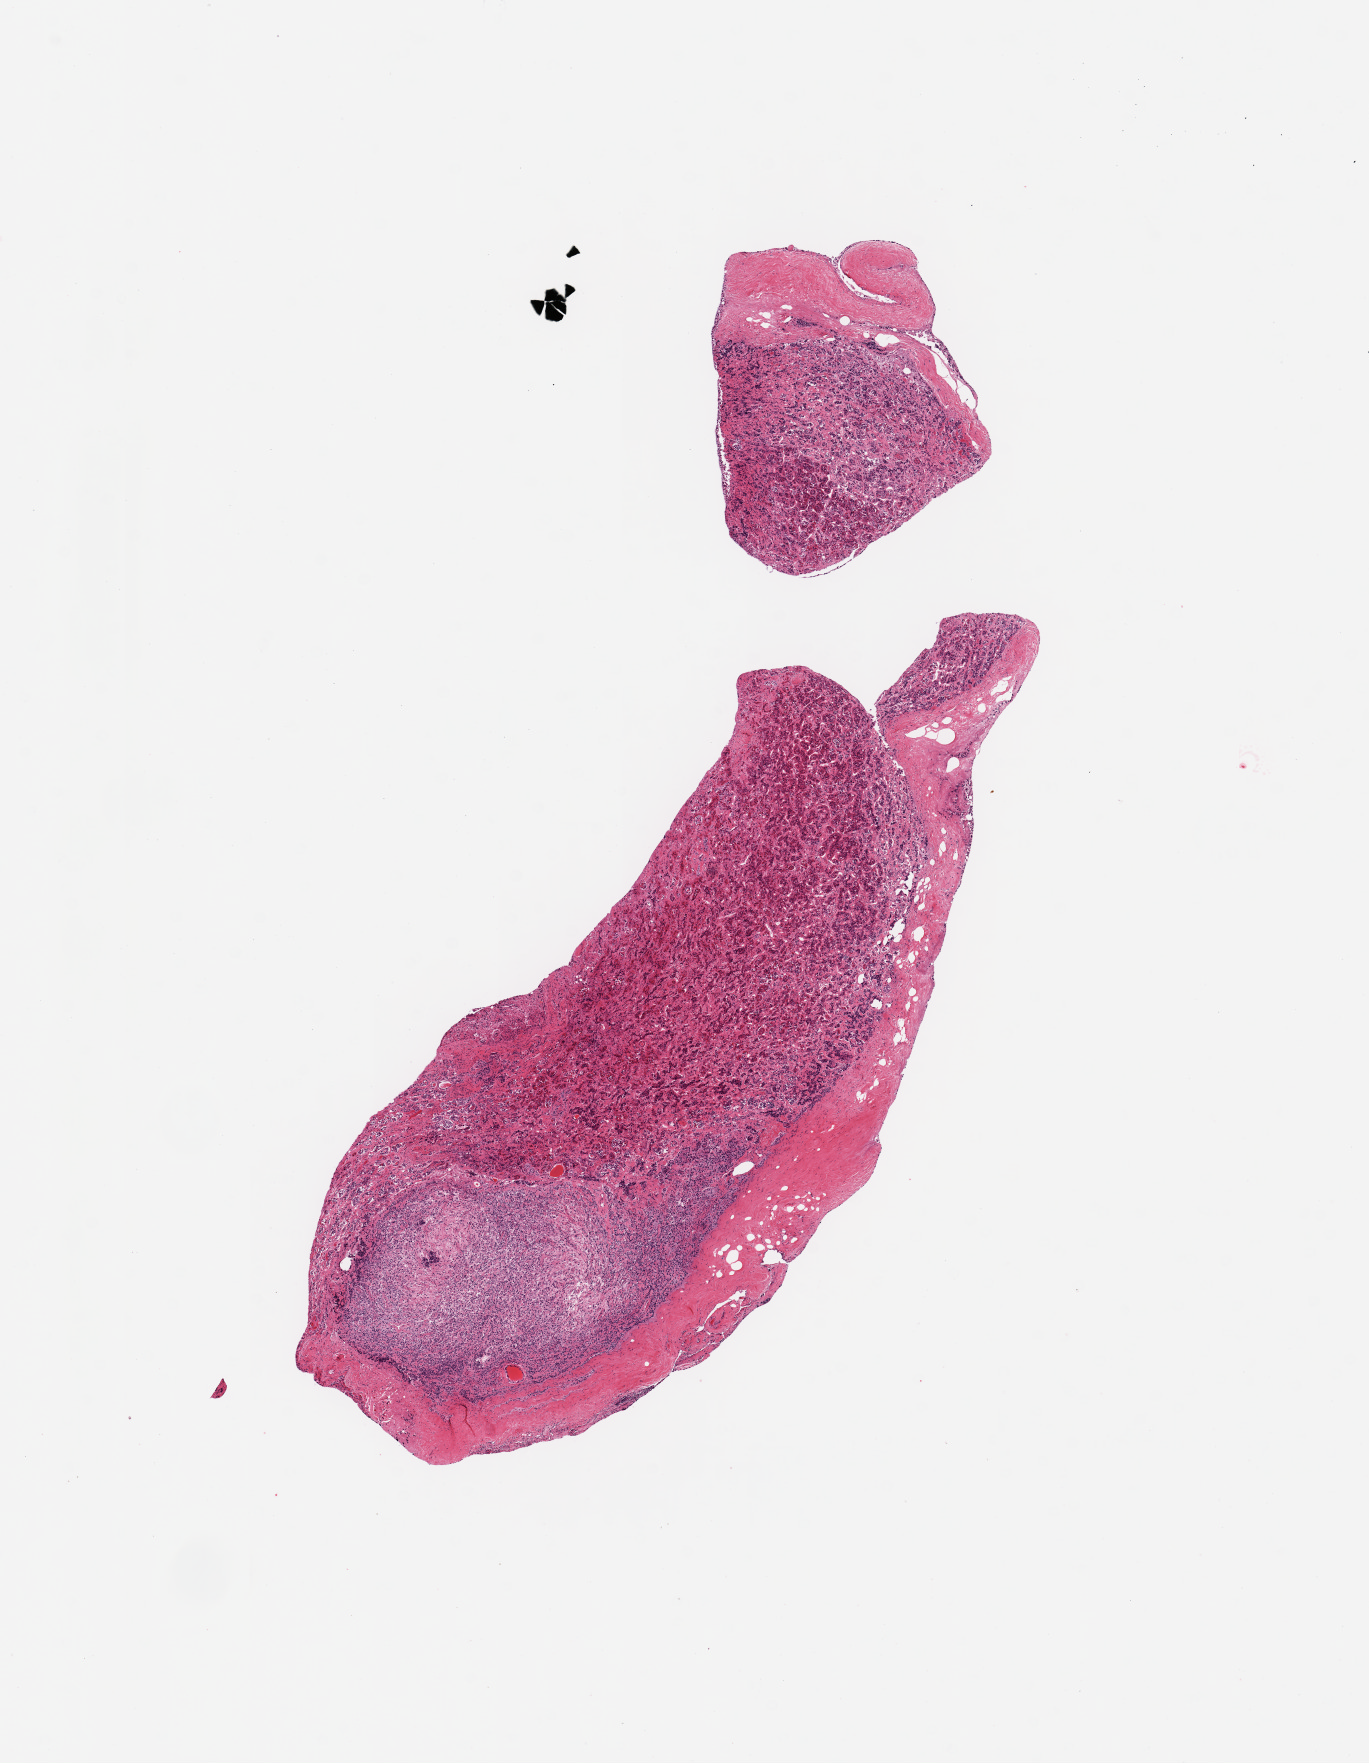
Digitized haematoxylin and eosin-stained section — low-resolution overview of the scanned area, about 10.8 x 13.9 mm, PAXgene-fixed, paraffin-embedded tissue, target tissue: pituitary, donor tissue sample. Donor: male.
Review note (as recorded): 1 piece (fragmented), adenohypophysis with ~4x1.5mm neurohypophysis, ~20% of specimen.